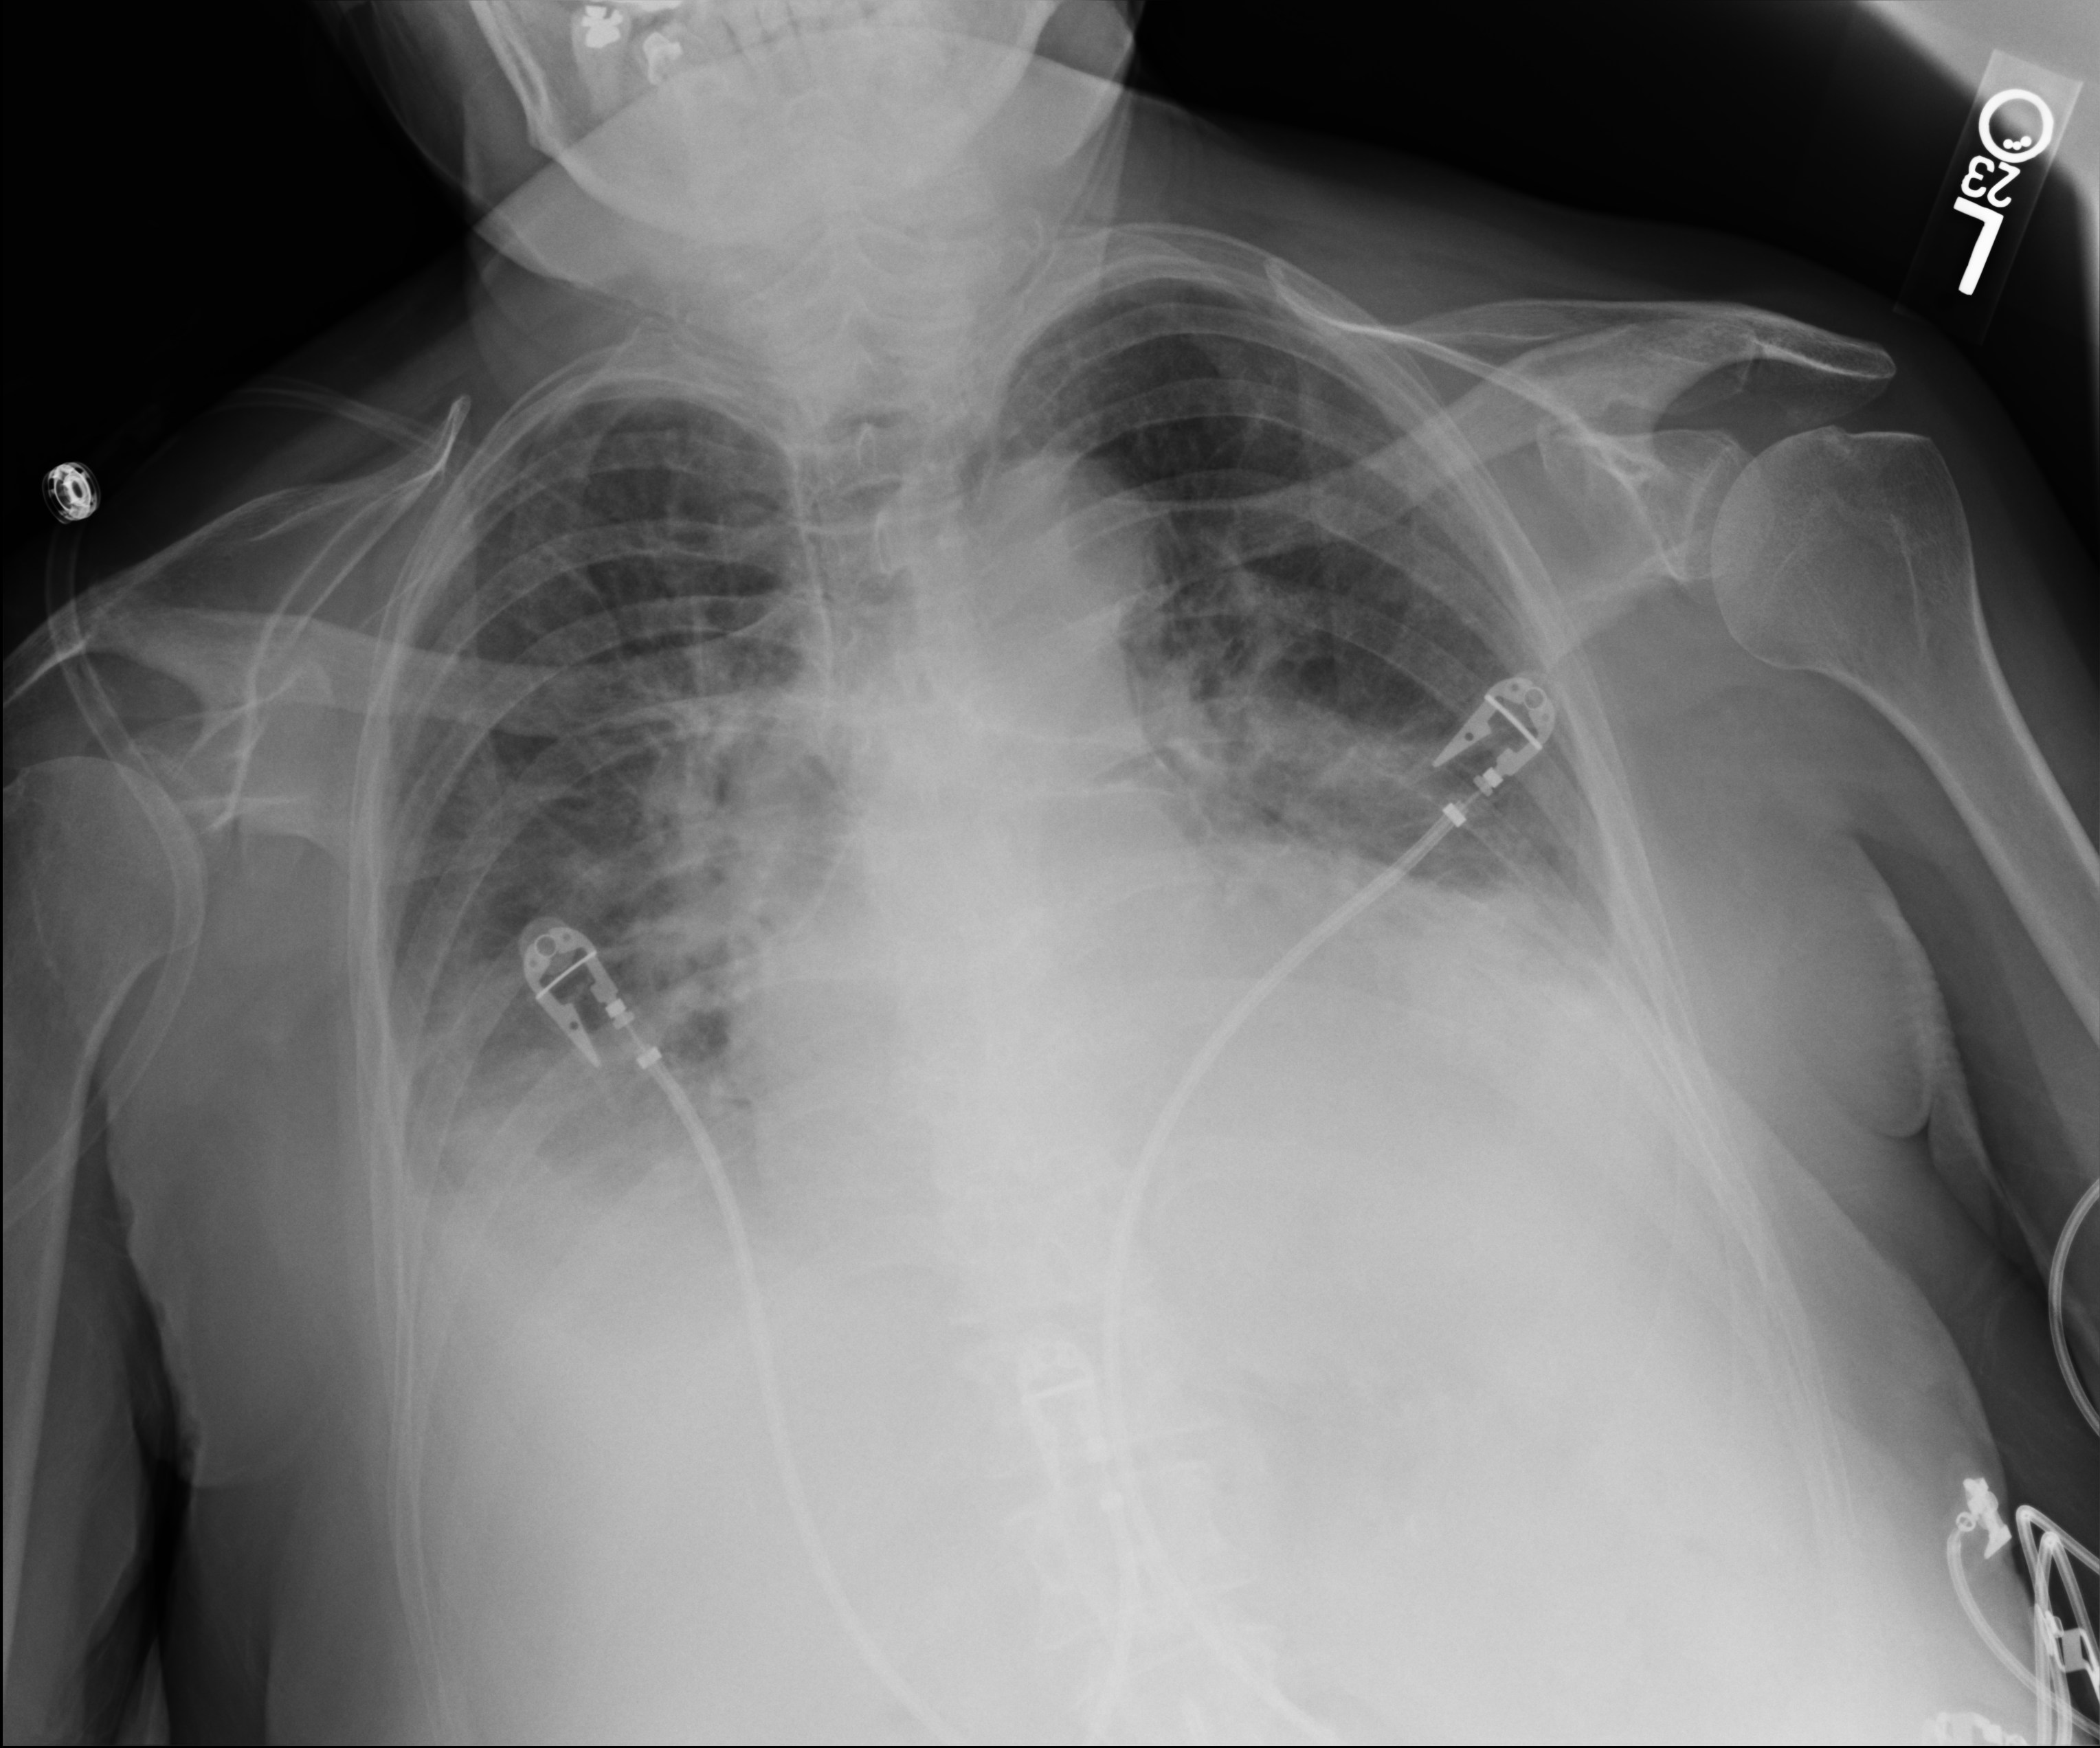
Chest X-ray (portable). Patient hospitalised with COVID-19; female, aged 75–90 years.
From the hospital-stay record, not from the radiograph (when in the stay this image was taken is not recorded): admitted to intensive care during this hospital stay: no.